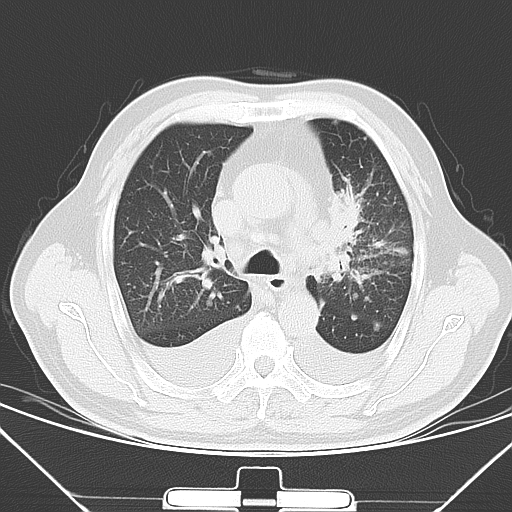
Chest CT, one axial slice; slice 43 of 66 in the series (ordered by position); lung window (W 1500 / L -600 HU); 5 mm slice thickness; 512 × 512 image matrix, field of view 352 × 352 mm. Patient: male, 66 years. From the clinical record (not read from this slice): clinical TNM (as recorded): T1c N0 M0.
Annotated regions visible in this slice (bounding box drawn by a radiologist):
- lung tumour (recorded histology: adenocarcinoma): bounding box (x1, y1, x2, y2) in pixels: (325, 187, 366, 248)